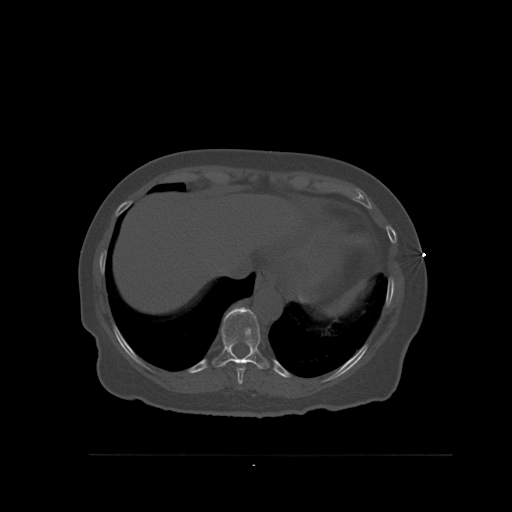
CT including the spine, one axial slice. Position 322 of 527 along the scan axis. Bone window (W 1800 / L 400 HU). 1.5 mm slice thickness. 512 × 512 image matrix, field of view 470 × 470 mm. Female patient, age 73 years. Case-level facts recorded for this patient, not image findings: primary cancer: breast; vertebrae with lytic lesions (as recorded): L2.
Outlined on this slice (semi-automatically segmented with operator editing):
- T10 vertebra: bounding box <212,307,270,370> (left, top, right, bottom; pixels)
- T9 vertebra: <237,364,246,385>